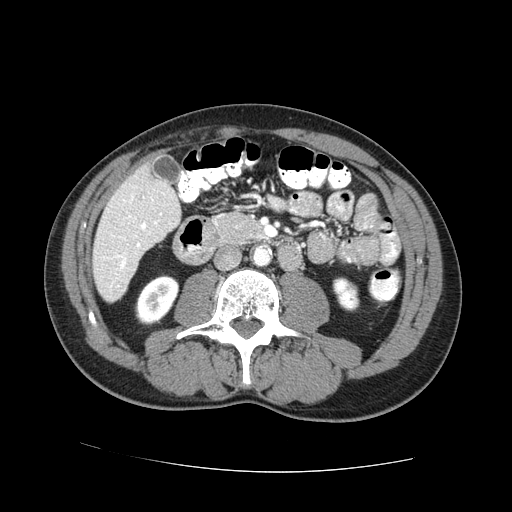
Contrast-enhanced abdominal CT (liver protocol), one axial slice; position 17 of 73 along the scan axis; 100 kVp; one of 2 acquisitions stored at this slice position; soft-tissue window (W 400 / L 40 HU); 2.5 mm slice thickness; 512 × 512 image matrix. Case-level facts recorded for this patient, not image findings: diagnosis: hepatocellular carcinoma (patient treated with transarterial chemoembolisation; whether this scan precedes or follows treatment is not stated here); TNM stage (as recorded): Stage-IVA; Child-Pugh class: A; tumour differentiation: no biopsy; tumour nodularity: uninodular.
Annotated regions visible in this slice (semi-automatically segmented with operator editing):
- liver parenchyma outside the tumour (the mass and vessels are separate outlines, so this box may not span the whole liver): bounding box [x1, y1, x2, y2] px = [92, 160, 180, 302]
- liver vessels: [114, 197, 161, 269]